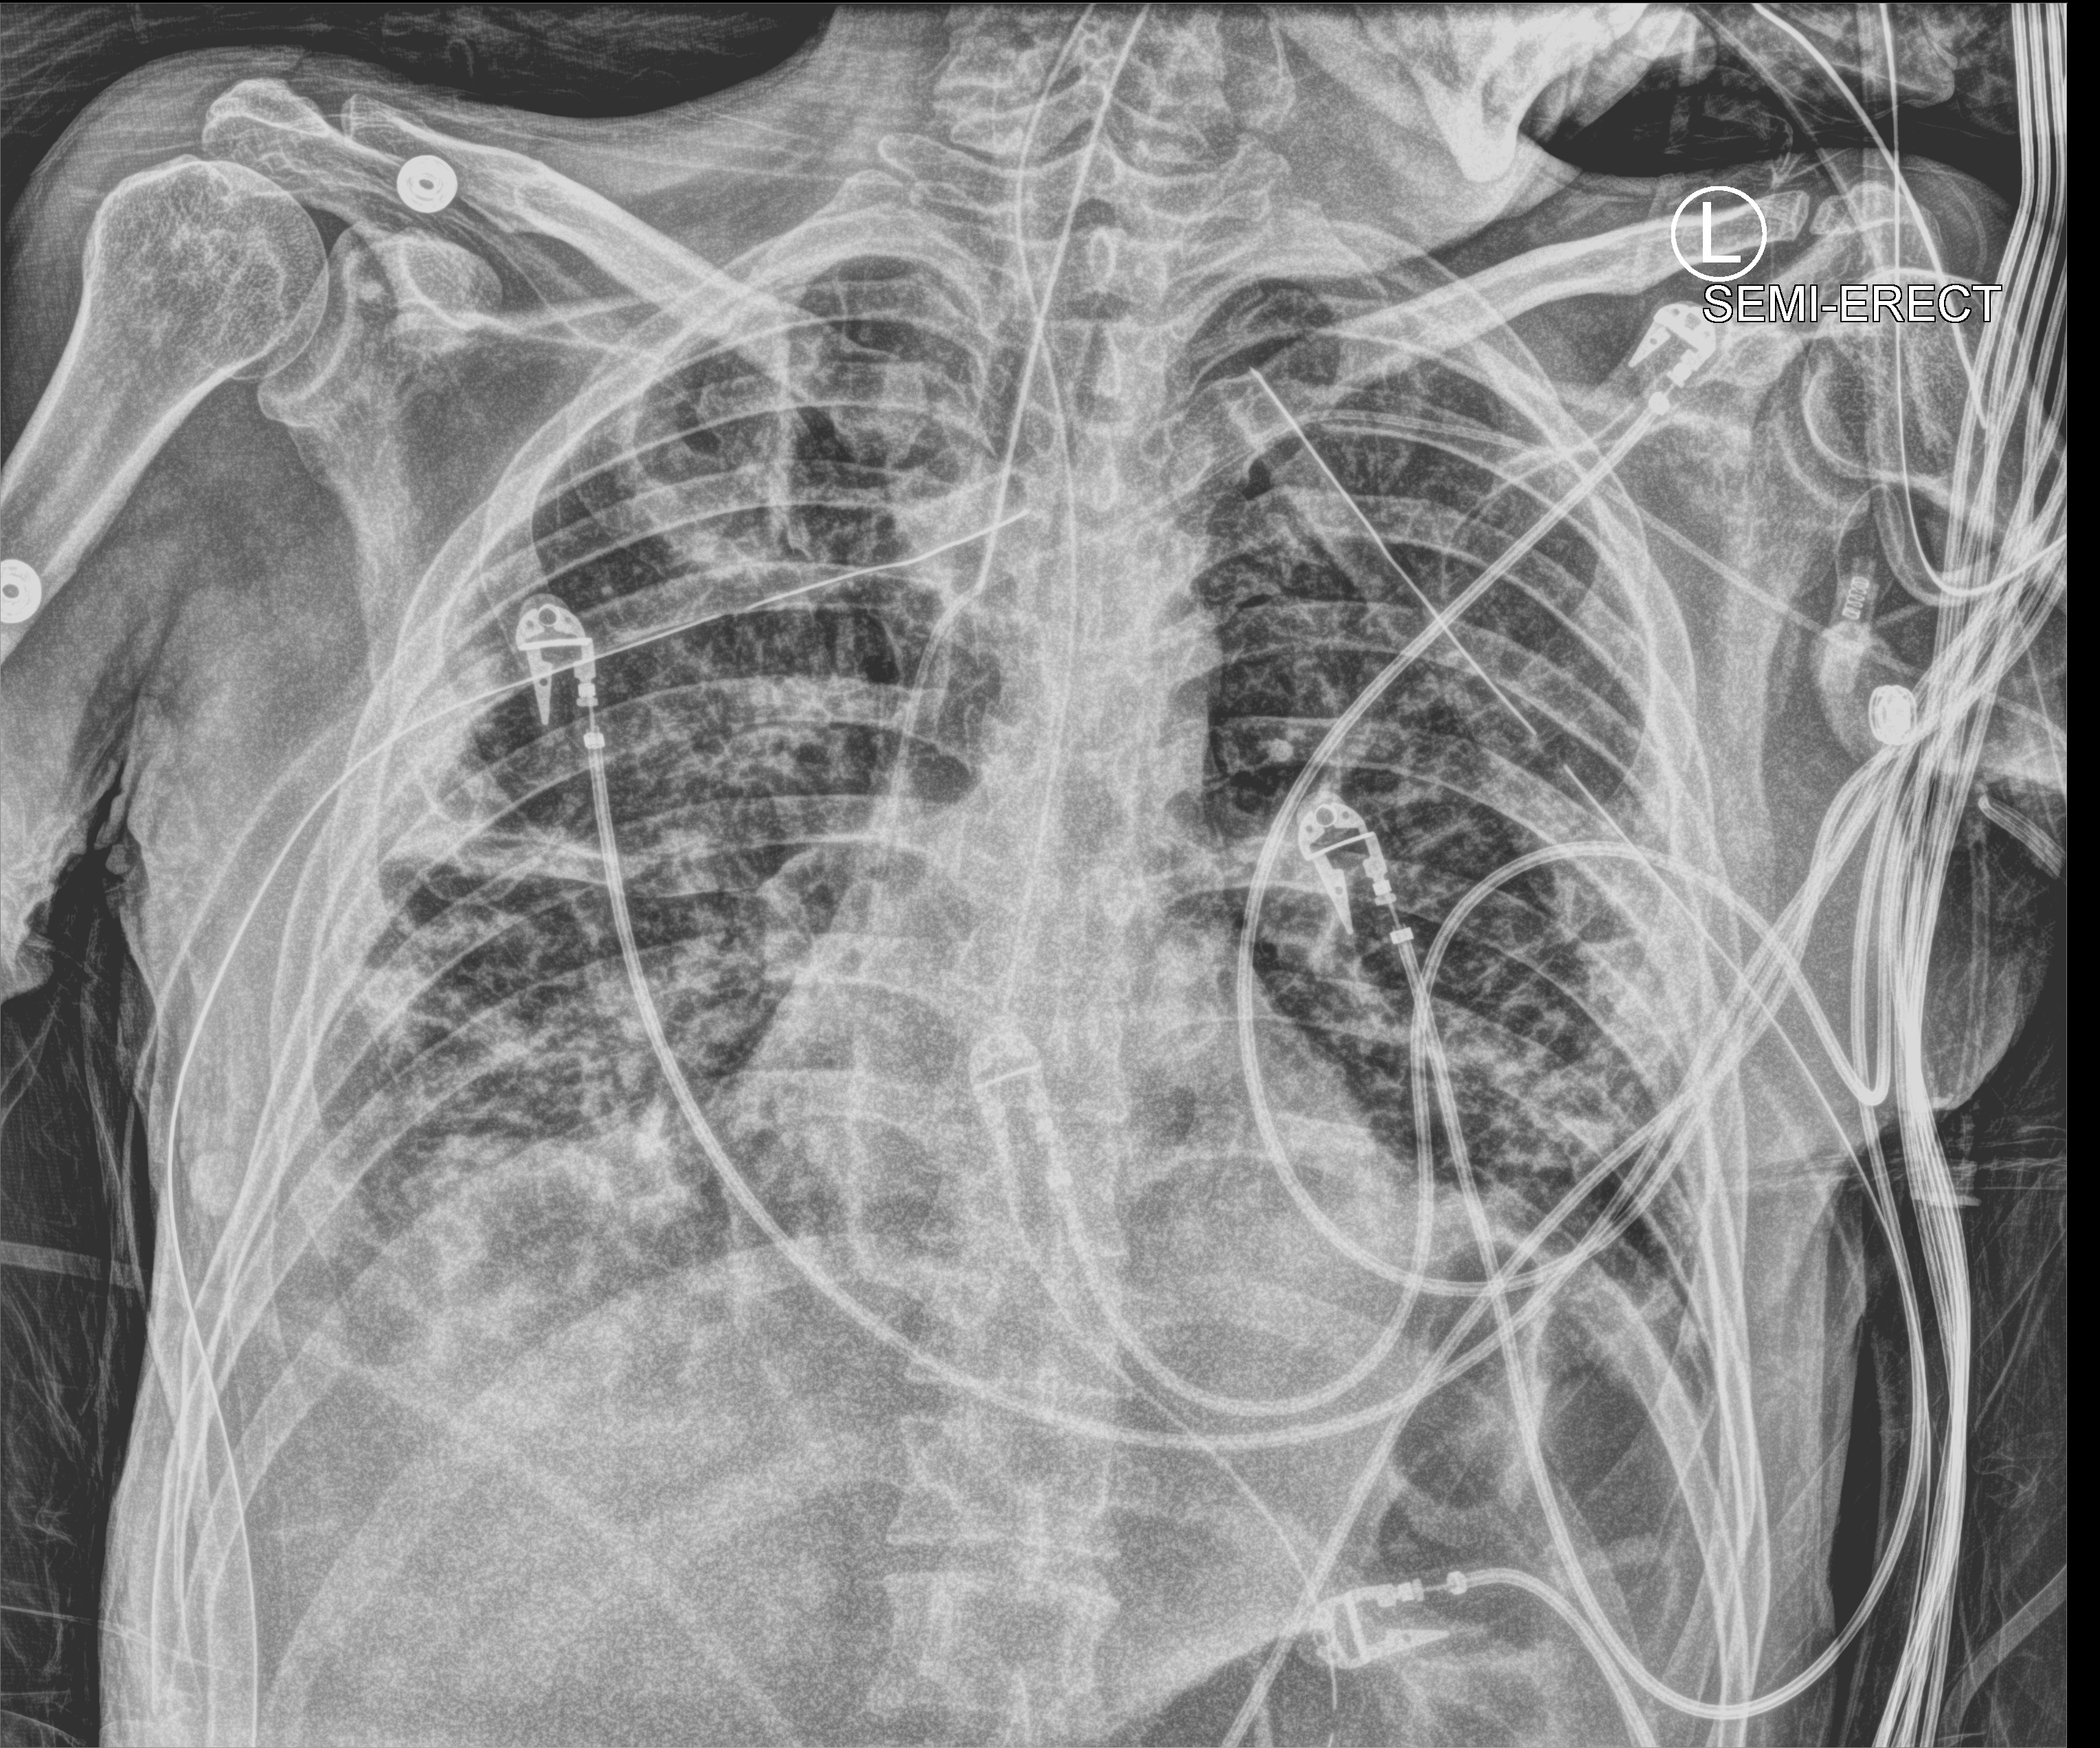
Chest X-ray (portable); anteroposterior (AP) projection. Patient hospitalised with COVID-19; male, aged 18–59 years.
Hospital-stay facts (about this admission, not read from this image; timing relative to this image not recorded): admitted to intensive care during this hospital stay: yes.